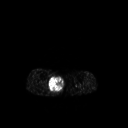
FDG PET of an extremity soft-tissue mass (from a PET/CT study), one axial slice. Slice 135 of 267 in the series (ordered by position). 3.27 mm slice thickness. 128 × 128 image matrix, field of view 500 × 500 mm. Male patient, age 69 years. Case-level facts recorded for this patient, not image findings: histological type: pleiomorphic liposarcoma; grade: high; site of the primary tumour: right calf.
Structures marked on this image (expert contour drawn on MRI and transferred to this co-registered scan by the dataset authors):
- gross tumour volume including surrounding oedema: bounding box (x1, y1, x2, y2) in pixels: (48, 74, 64, 95)
- gross tumour volume (mass): (48, 76, 64, 91)